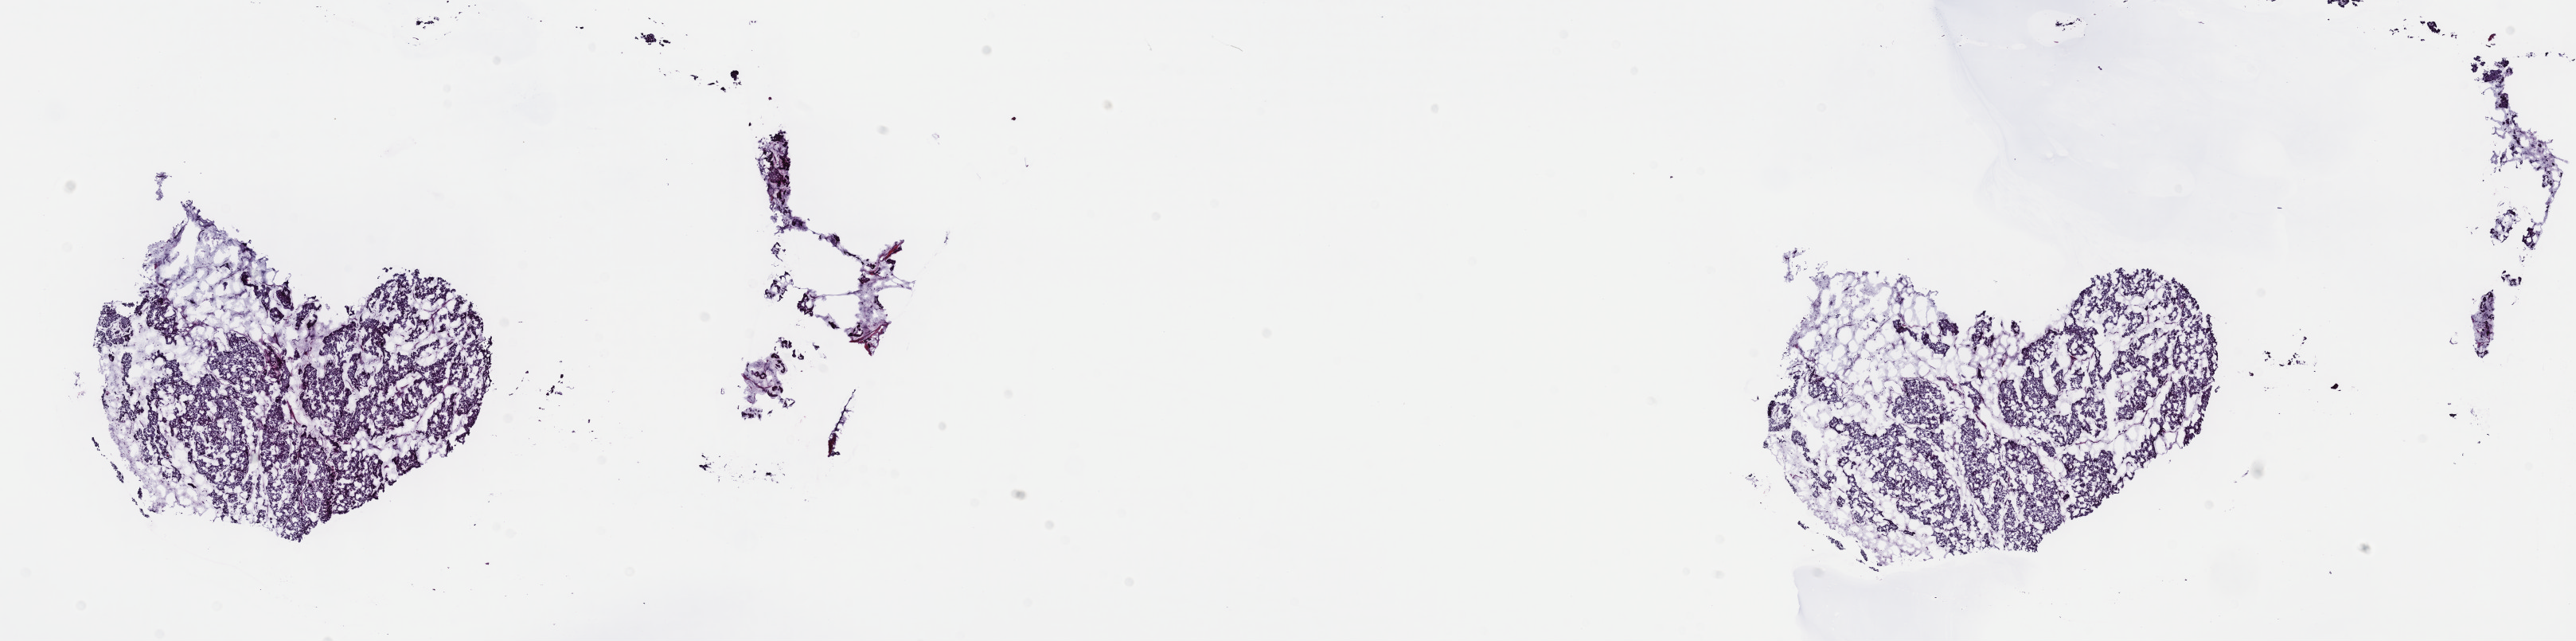
H&E-stained whole-slide image, a low-resolution overview of the entire scanned area, about 26.2 x 6.5 mm; frozen section; breast, primary tumour sample. Female, age 52 years at initial diagnosis. Pathologist review of this section (percent, as recorded): tumour cells 75%, tumour nuclei 75%.
Diagnosis: Infiltrating duct mixed with other types of carcinoma.